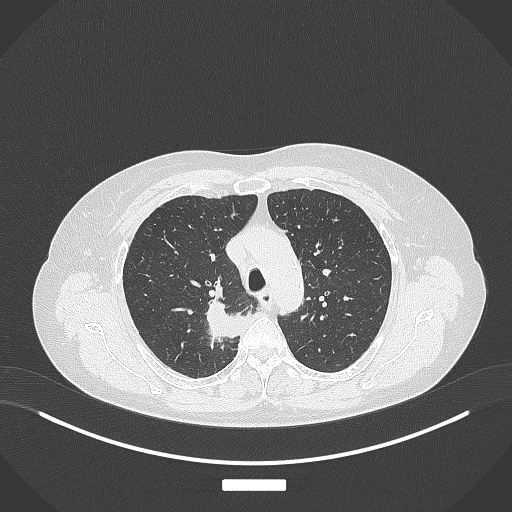
Chest CT, one axial slice. 120 kVp. Lung window (W 1500 / L -600 HU). 512 × 512 image matrix. Patient: female, 62 years. Case-level facts recorded for this patient, not image findings: clinical TNM (as recorded): T1c N1 M0.
Structures marked on this image (rectangle marked by the reading radiologist):
- lung tumour (recorded histology: squamous cell carcinoma): bounding box [x1, y1, x2, y2] px = [203, 299, 250, 342]